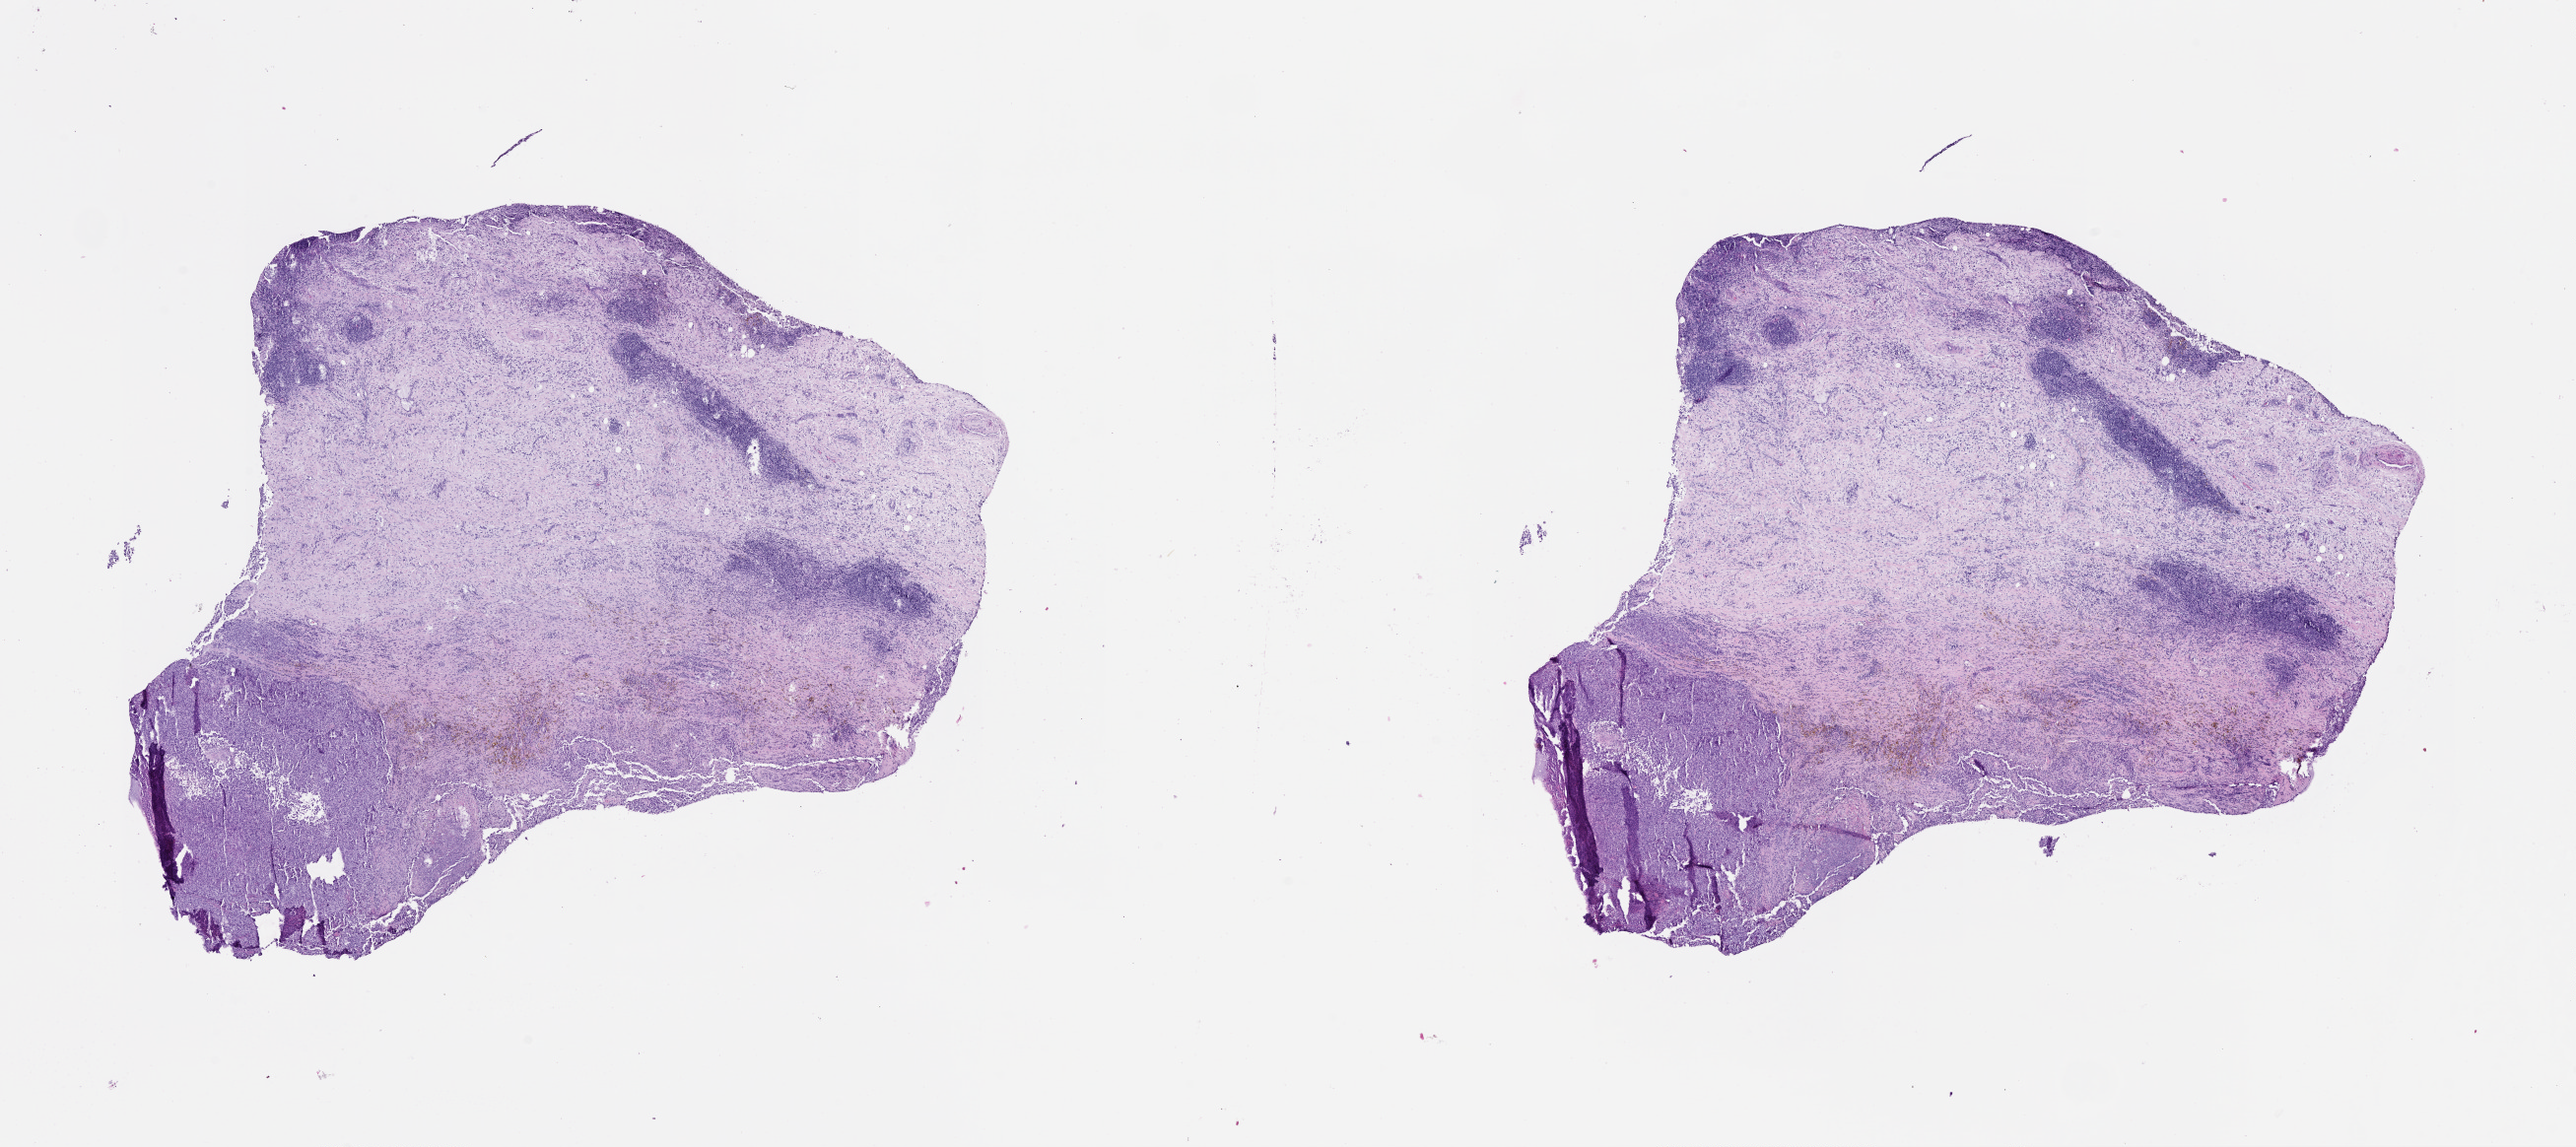
Whole-slide histology image, H&E — shown as a low-resolution overview of the whole scanned area (about 21.0 x 9.4 mm, from a 20x scan). Male, 72 y/o.
Patient diagnosis: Malignant melanoma, NOS.